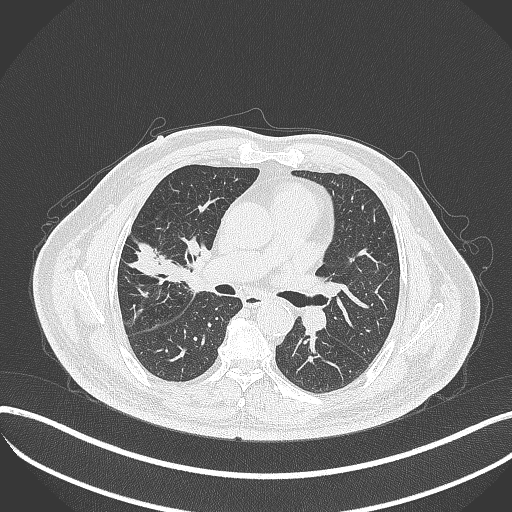
Chest CT, one axial slice; position 204 of 401 along the scan axis; reconstruction kernel B70f; lung window (W 1500 / L -600 HU); 1 mm slice thickness; 512 × 512 image matrix, field of view 400 × 400 mm. Patient: male, 72 years. From the clinical record (not read from this slice): clinical TNM (as recorded): T1c N0 M0.
Structures marked on this image (rectangle marked by the reading radiologist):
- lung tumour (recorded histology: squamous cell carcinoma): box from (x=172, y=236) to (x=213, y=301) px